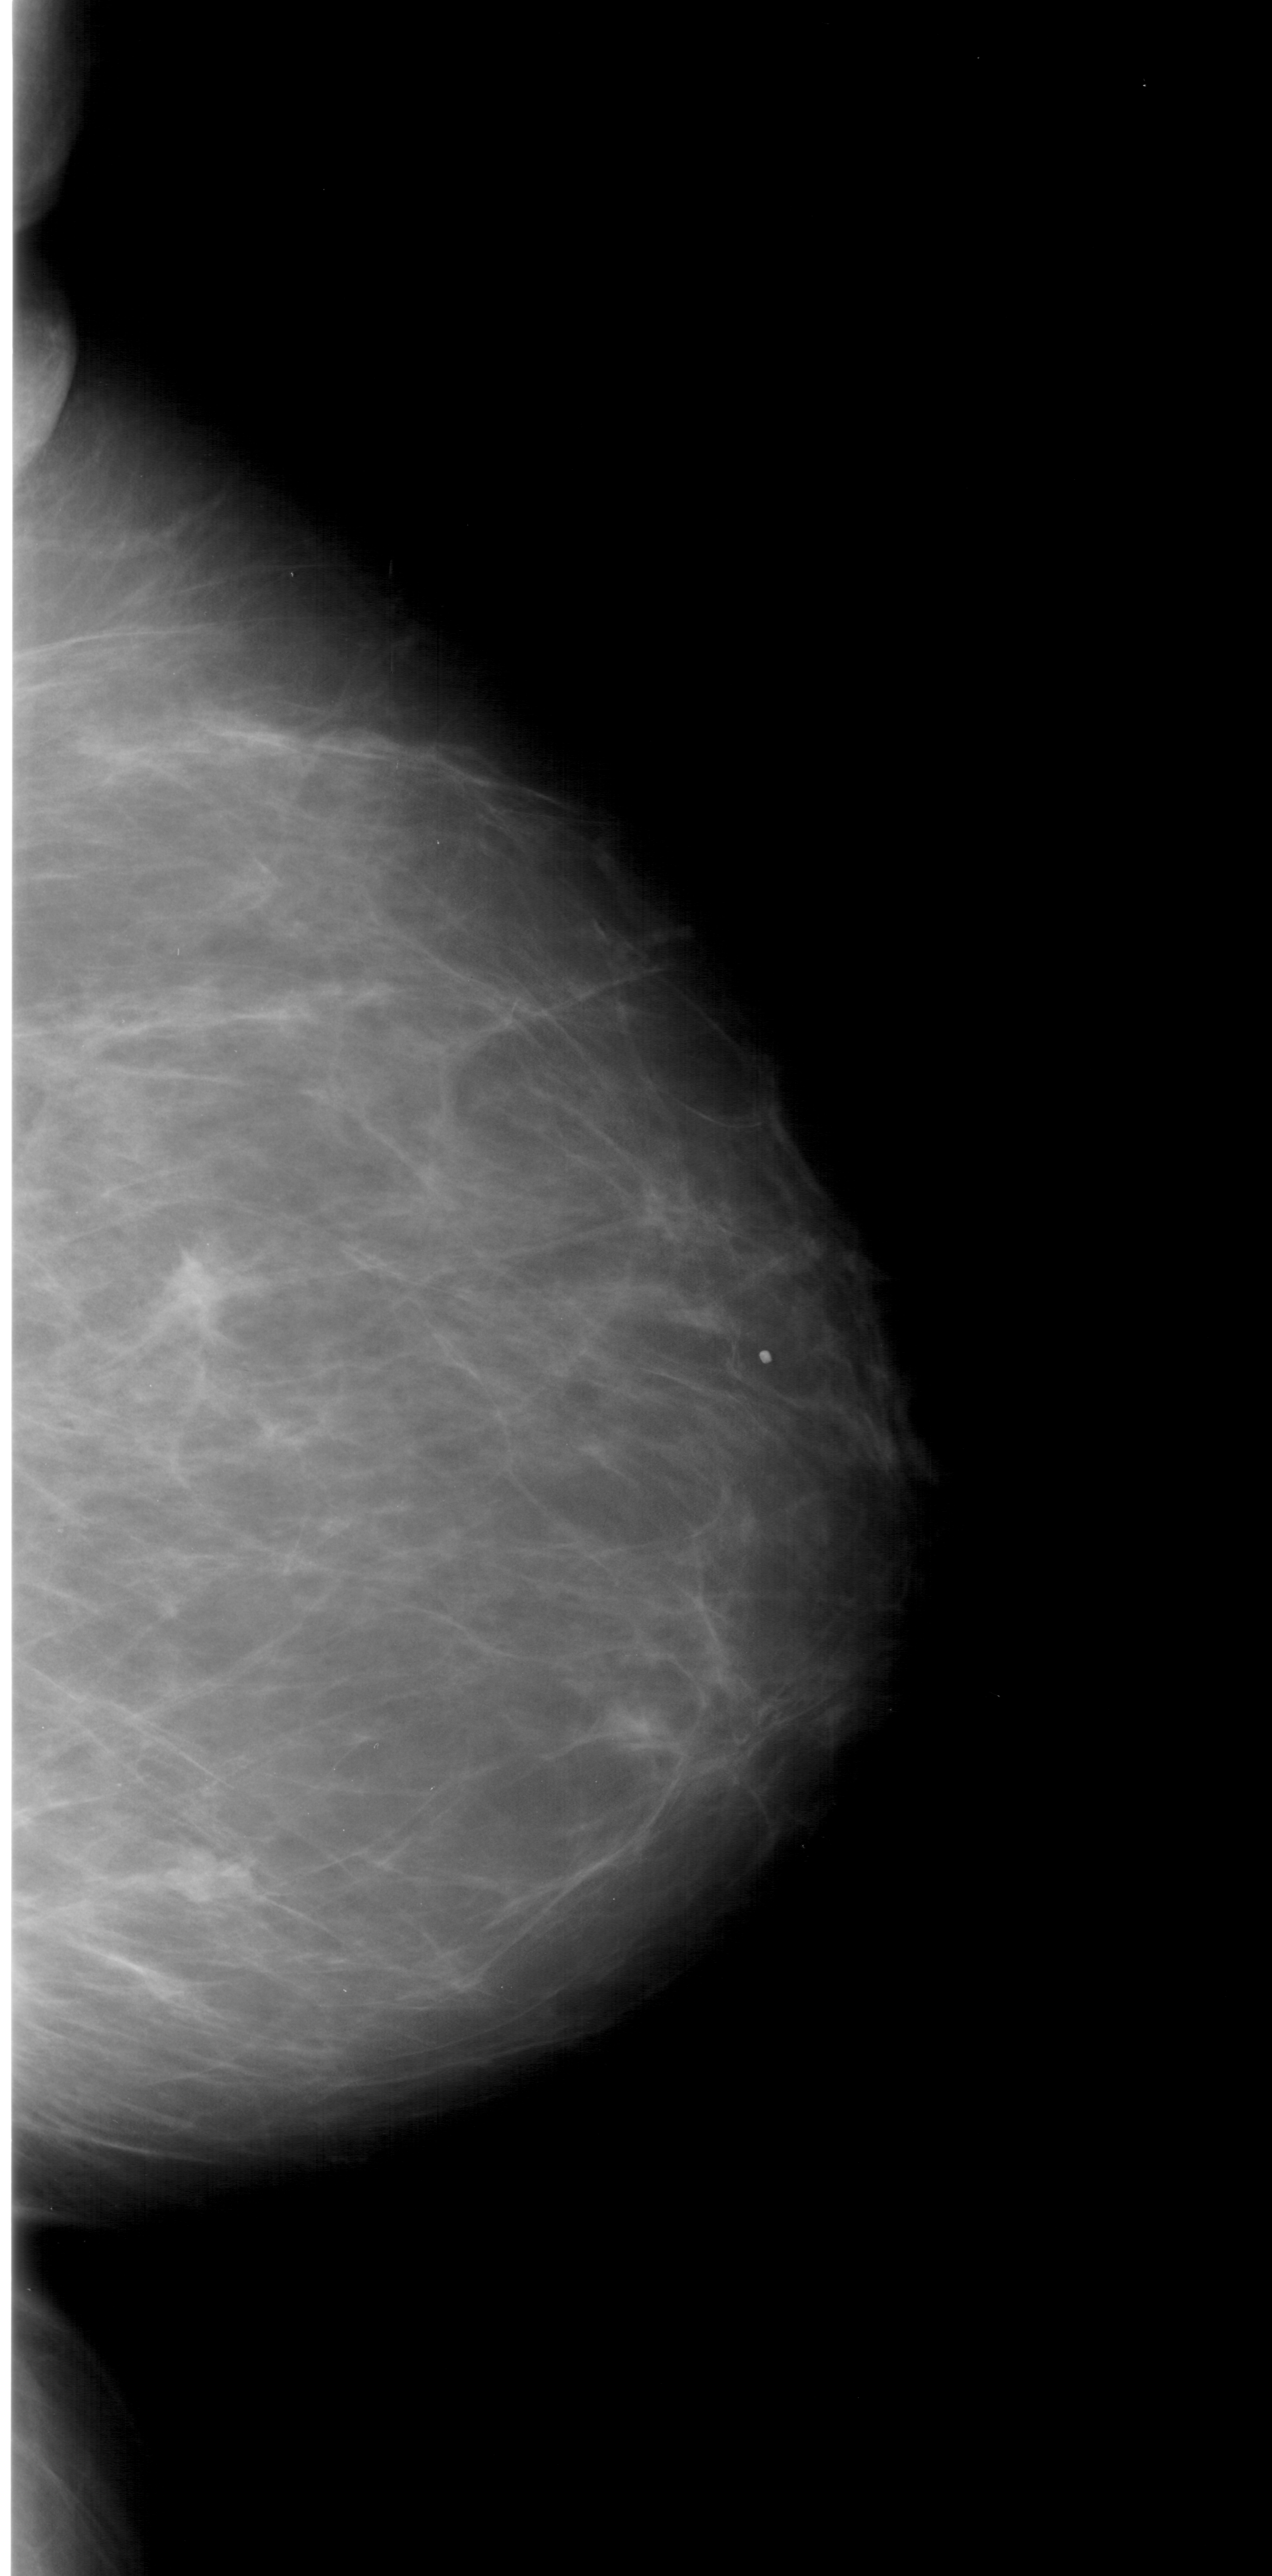
Mammogram (digitized film). Right breast. Craniocaudal (CC) view. Breast composition: heterogeneously dense (BI-RADS density category 3 of 4). 1272 × 2576 image matrix.
Expert-marked regions of interest on this image (one box per marked abnormality):
- mass, shape irregular, margins spiculated; BI-RADS assessment category 5; pathology (as recorded): malignant: box from (x=141, y=1230) to (x=257, y=1349) px